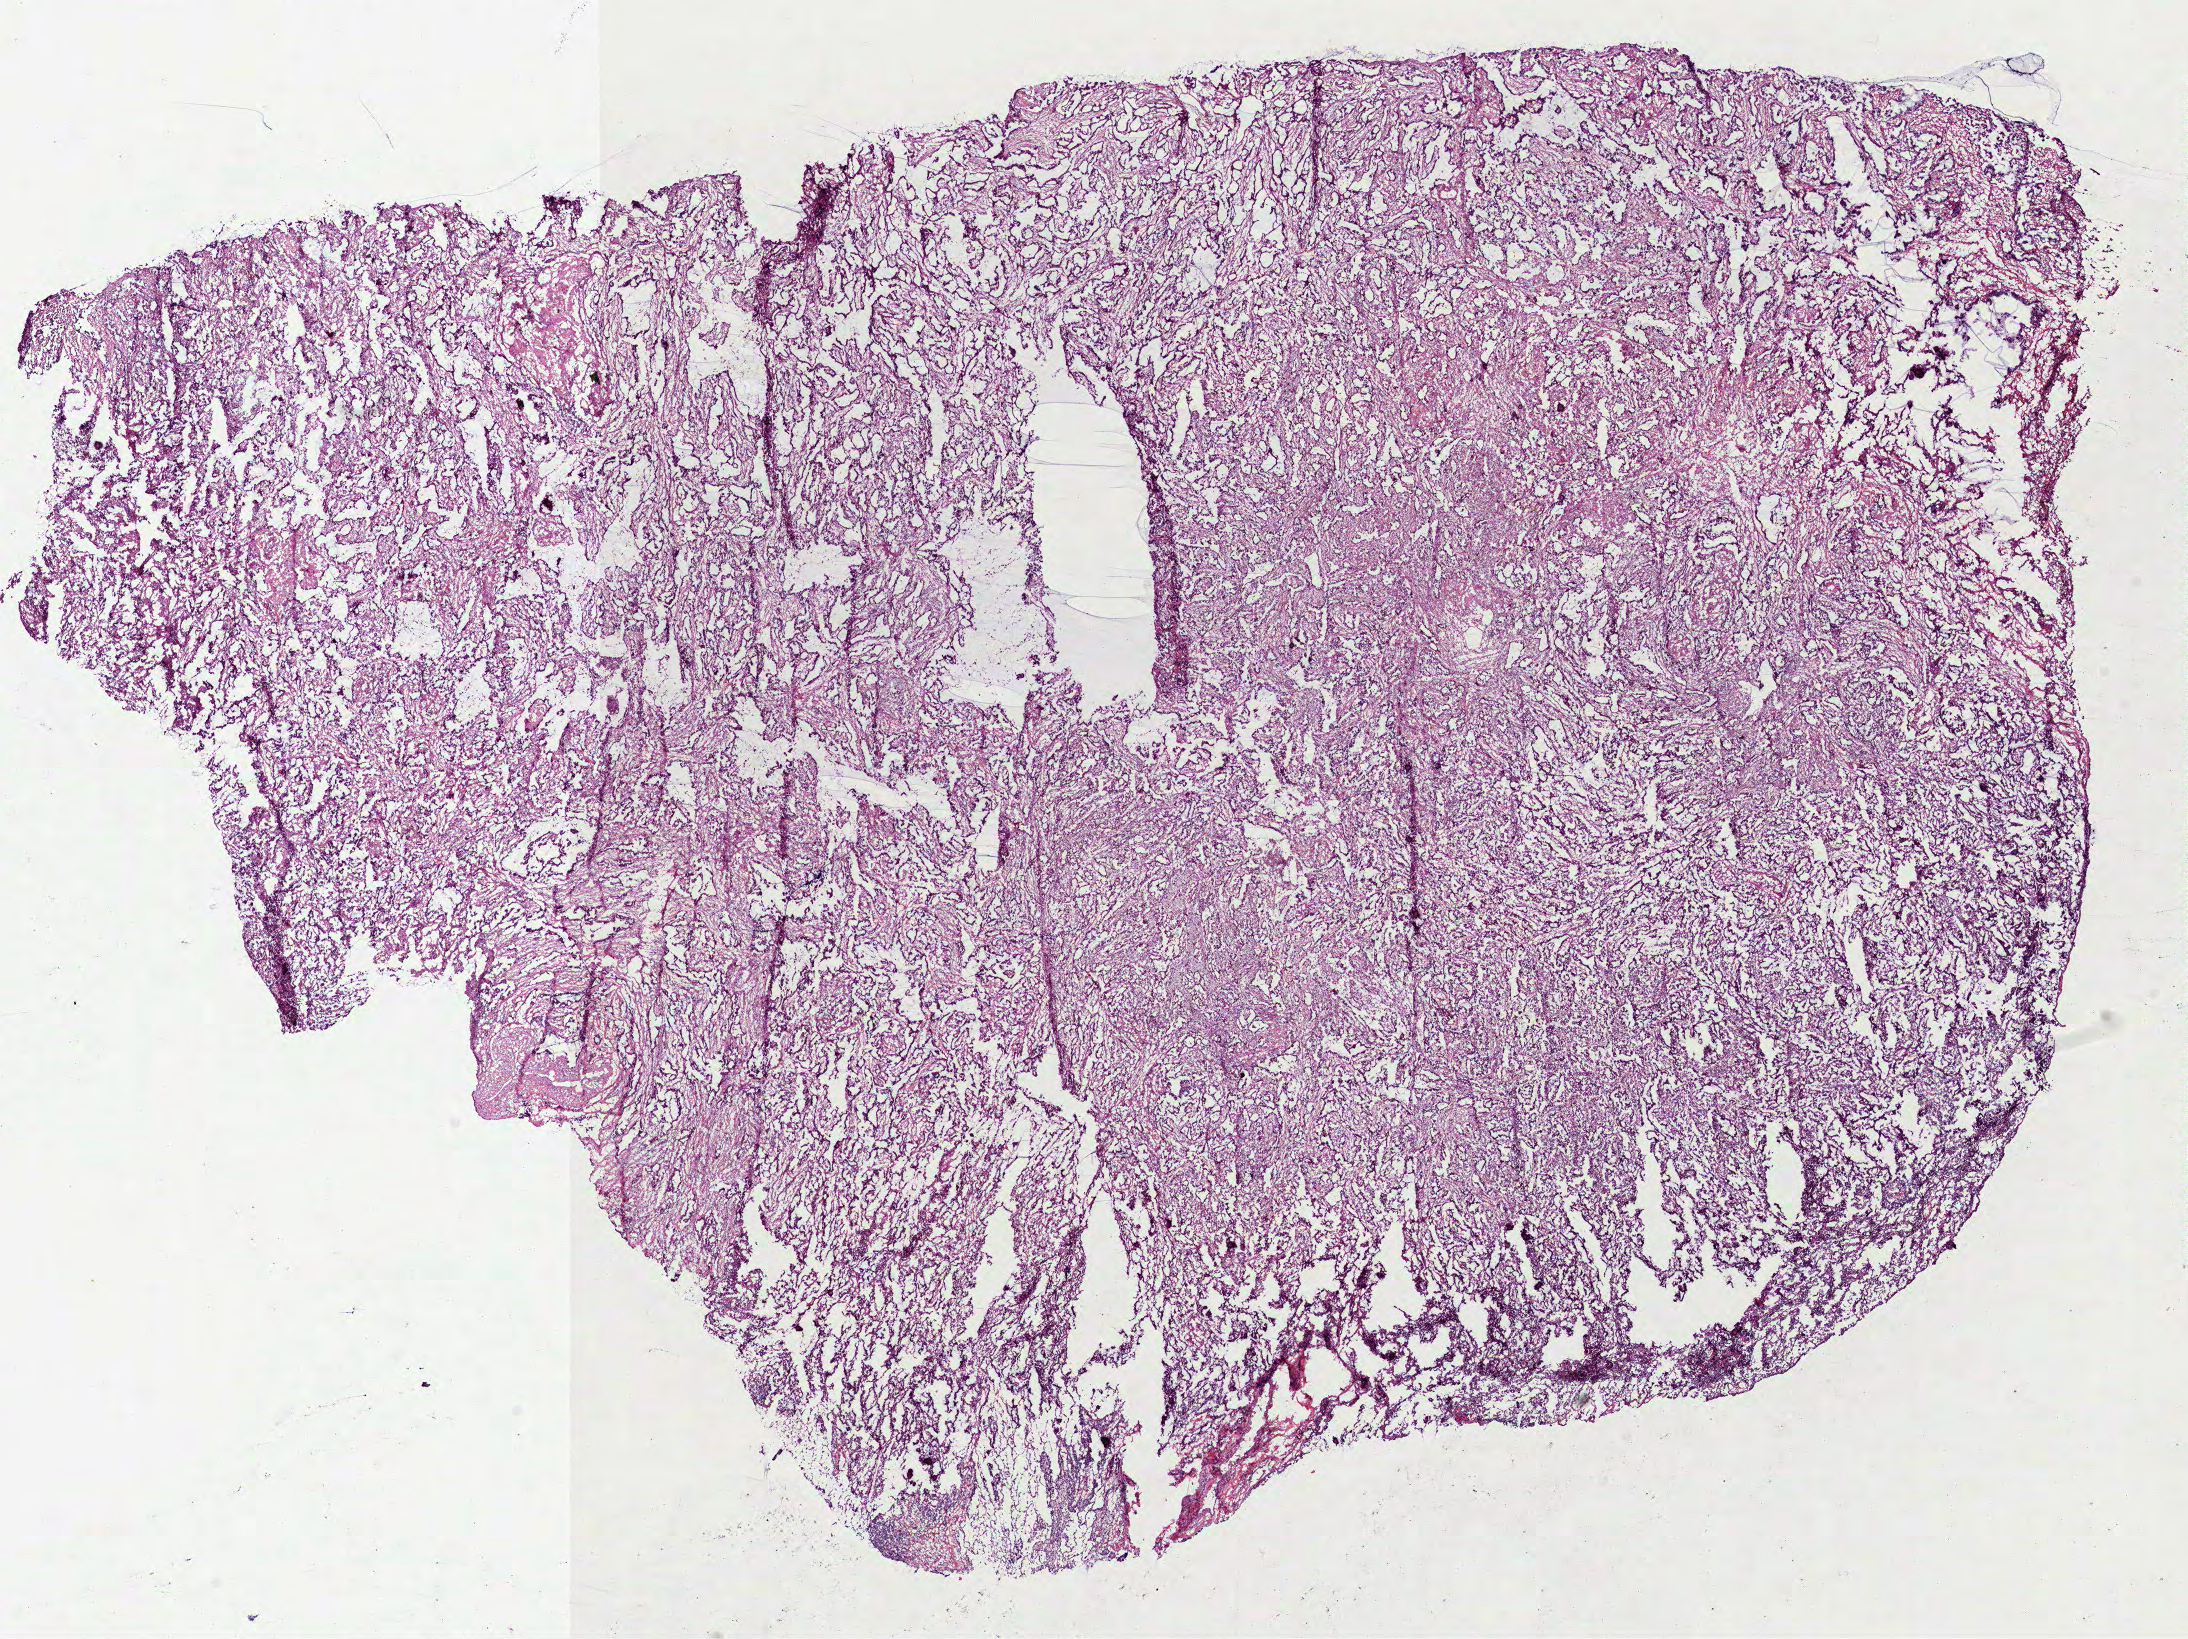
Whole-slide histology image, H&E-stained, whole scanned area (about 17.6 x 13.2 mm) shown as a low-resolution overview. Frozen section. Primary tumour sample from the lung. Female, age 63 years at initial diagnosis. Slide review estimates, as recorded: tumour cells 85%, tumour nuclei 80%, normal cells 0%, stromal cells 15%, necrosis 0%.
• AJCC pathologic stage: IIB (7th edition)
• histologic diagnosis: Mucinous adenocarcinoma (lower lobe, lung)